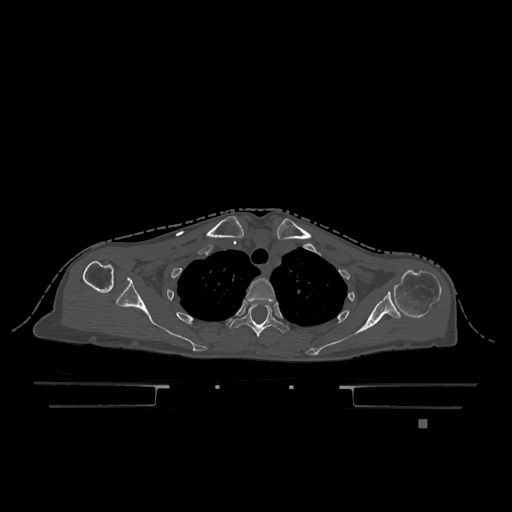
CT including the spine, one axial slice; position 936 of 1317 along the scan axis; bone window (W 1800 / L 400 HU); 0.5 mm slice thickness; 512 × 512 image matrix. Patient: female, 74 years. From the clinical record (not read from this slice): primary cancer: lung.
Outlined on this slice (semi-automatically segmented with operator editing):
- T2 vertebra: box from (x=246, y=278) to (x=275, y=302) px
- T3 vertebra: (x=230, y=304)–(x=289, y=337)